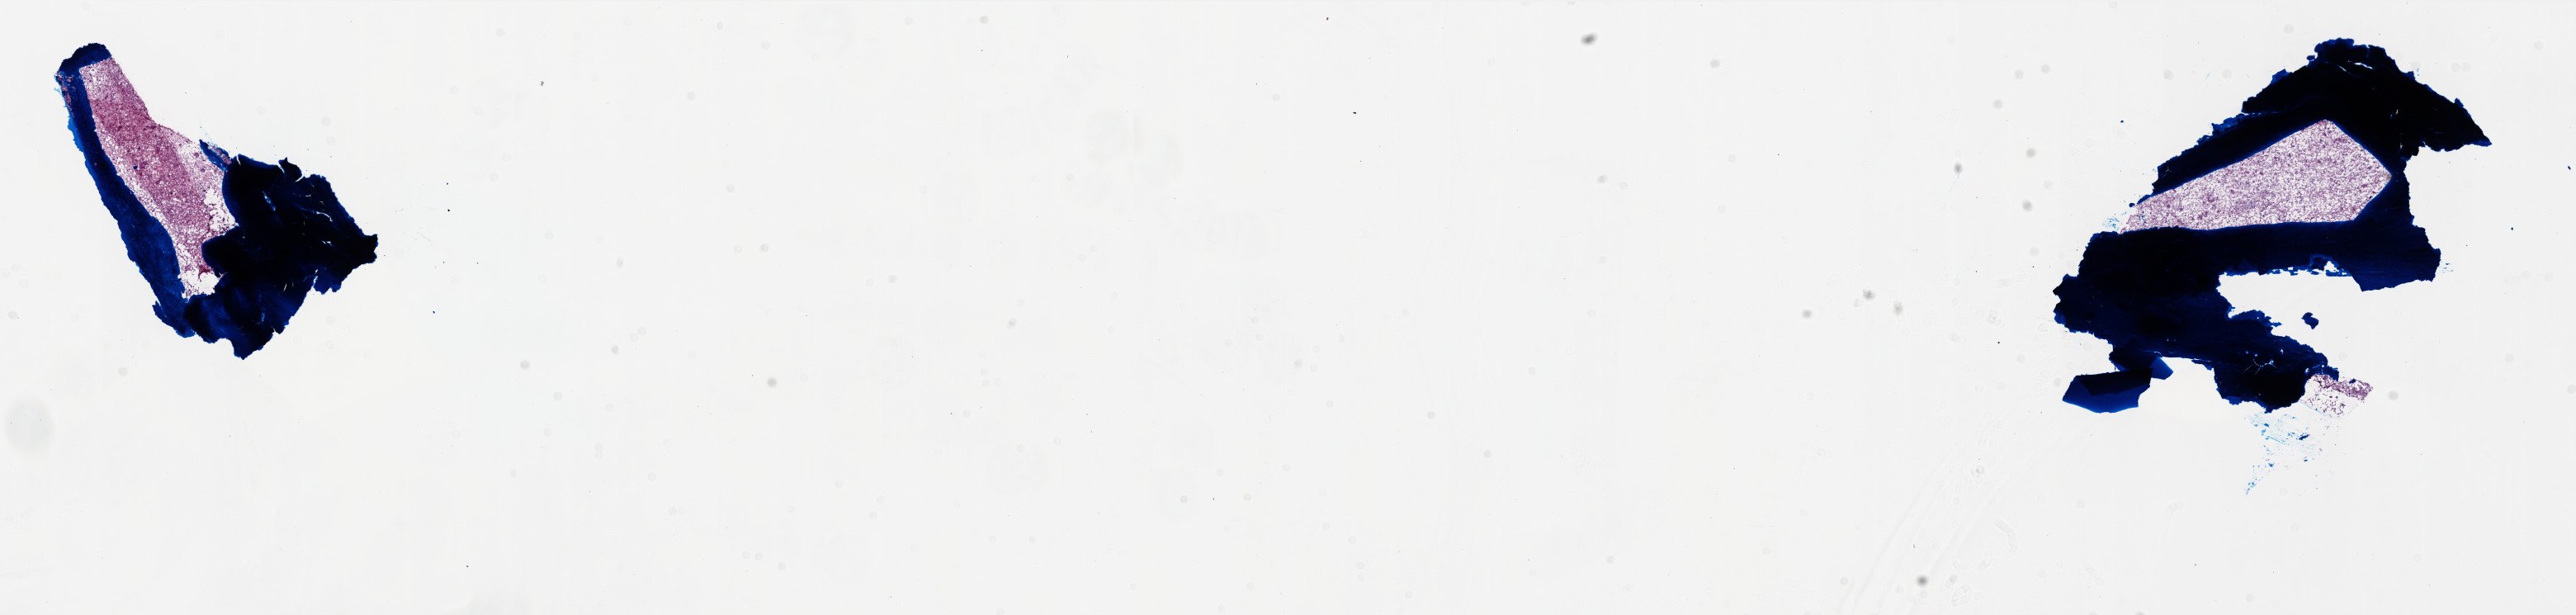
Whole-slide histology image, H&E, whole scanned area (about 25.0 x 6.0 mm) shown as a low-resolution overview, frozen section from the top of the tissue portion, sample: primary tumour, brain. Female, age 55 years at initial diagnosis. Composition of this section per pathologist review: tumour cells 50%, tumour nuclei 95%, normal cells 0%, stromal cells 5%, necrosis 45%.
• diagnosis: Glioblastoma